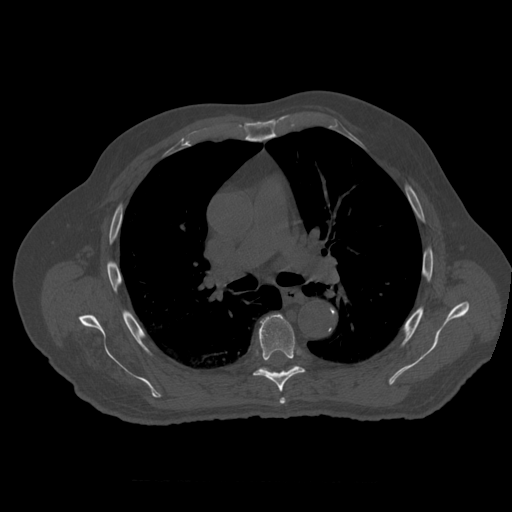
CT including the spine, one axial slice. Position 381 of 399 along the scan axis. 120 kVp. Bone window (W 1800 / L 400 HU). 1.25 mm slice thickness. 512 × 512 image matrix, field of view 407 × 407 mm. Patient age 73 years. From the clinical record (not read from this slice): primary cancer: prostate.
Structures marked on this image (semi-automatically segmented with operator editing):
- T5 vertebra: bounding box <280,398,286,404> (left, top, right, bottom; pixels)
- T6 vertebra: <254,314,305,393>